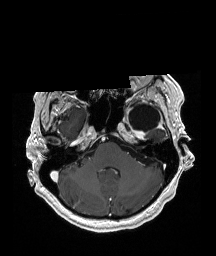
Brain MRI from a brain-tumour surgery series, one axial slice. Position 144 of 192 along the scan axis. T1-weighted post-contrast. 1 mm slice thickness. 216 × 256 image matrix, field of view 211 × 250 mm. Case-level facts recorded for this patient, not image findings: histopathology: Glioblastoma; WHO grade: 4; IDH mutation: no.
Annotated regions visible in this slice (outlined manually by an expert reader):
- previous resection cavity: bounding box (x1, y1, x2, y2) in pixels: (129, 104, 160, 132)